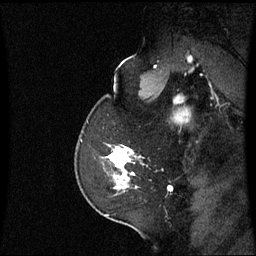
Breast MRI (dynamic contrast-enhanced), one sagittal slice; slice 46 of 60 in the series (ordered by position); dynamic contrast-enhanced series, image 2 of 3 at this slice position (ordered by acquisition); 1.5 T; TE 4.2 ms, TR 8.9 ms; 2.2 mm slice thickness; 256 × 256 image matrix, field of view 220 × 220 mm. Female patient, age 58 years. From the clinical record (not read from this slice): setting: breast cancer imaged before/during neoadjuvant chemotherapy; receptor status: triple-negative.
Annotated regions visible in this slice (semi-automatic segmentation, software-assisted and operator-edited):
- analysis volume of interest (the breast-tissue region the enhancement analysis was run in; not a lesion): bounding box (x1, y1, x2, y2) in pixels: (102, 146, 141, 191)
- tumour enhancement mask (voxels above the 70 % enhancement threshold inside the analysis volume of interest): (108, 148, 135, 183)